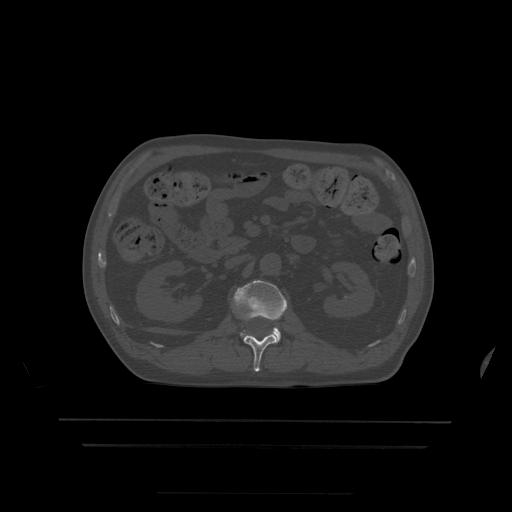
CT including the spine, one axial slice; slice 159 of 522 in the series (ordered by position); bone window (W 1800 / L 400 HU); 512 × 512 image matrix, field of view 436 × 436 mm. Patient age 68 years. From the clinical record (not read from this slice): primary cancer: urothelial.
Annotated regions visible in this slice (semi-automatic segmentation, software-assisted and operator-edited):
- L1 vertebra: bounding box <244,334,278,372> (left, top, right, bottom; pixels)
- L2 vertebra: <234,280,288,342>